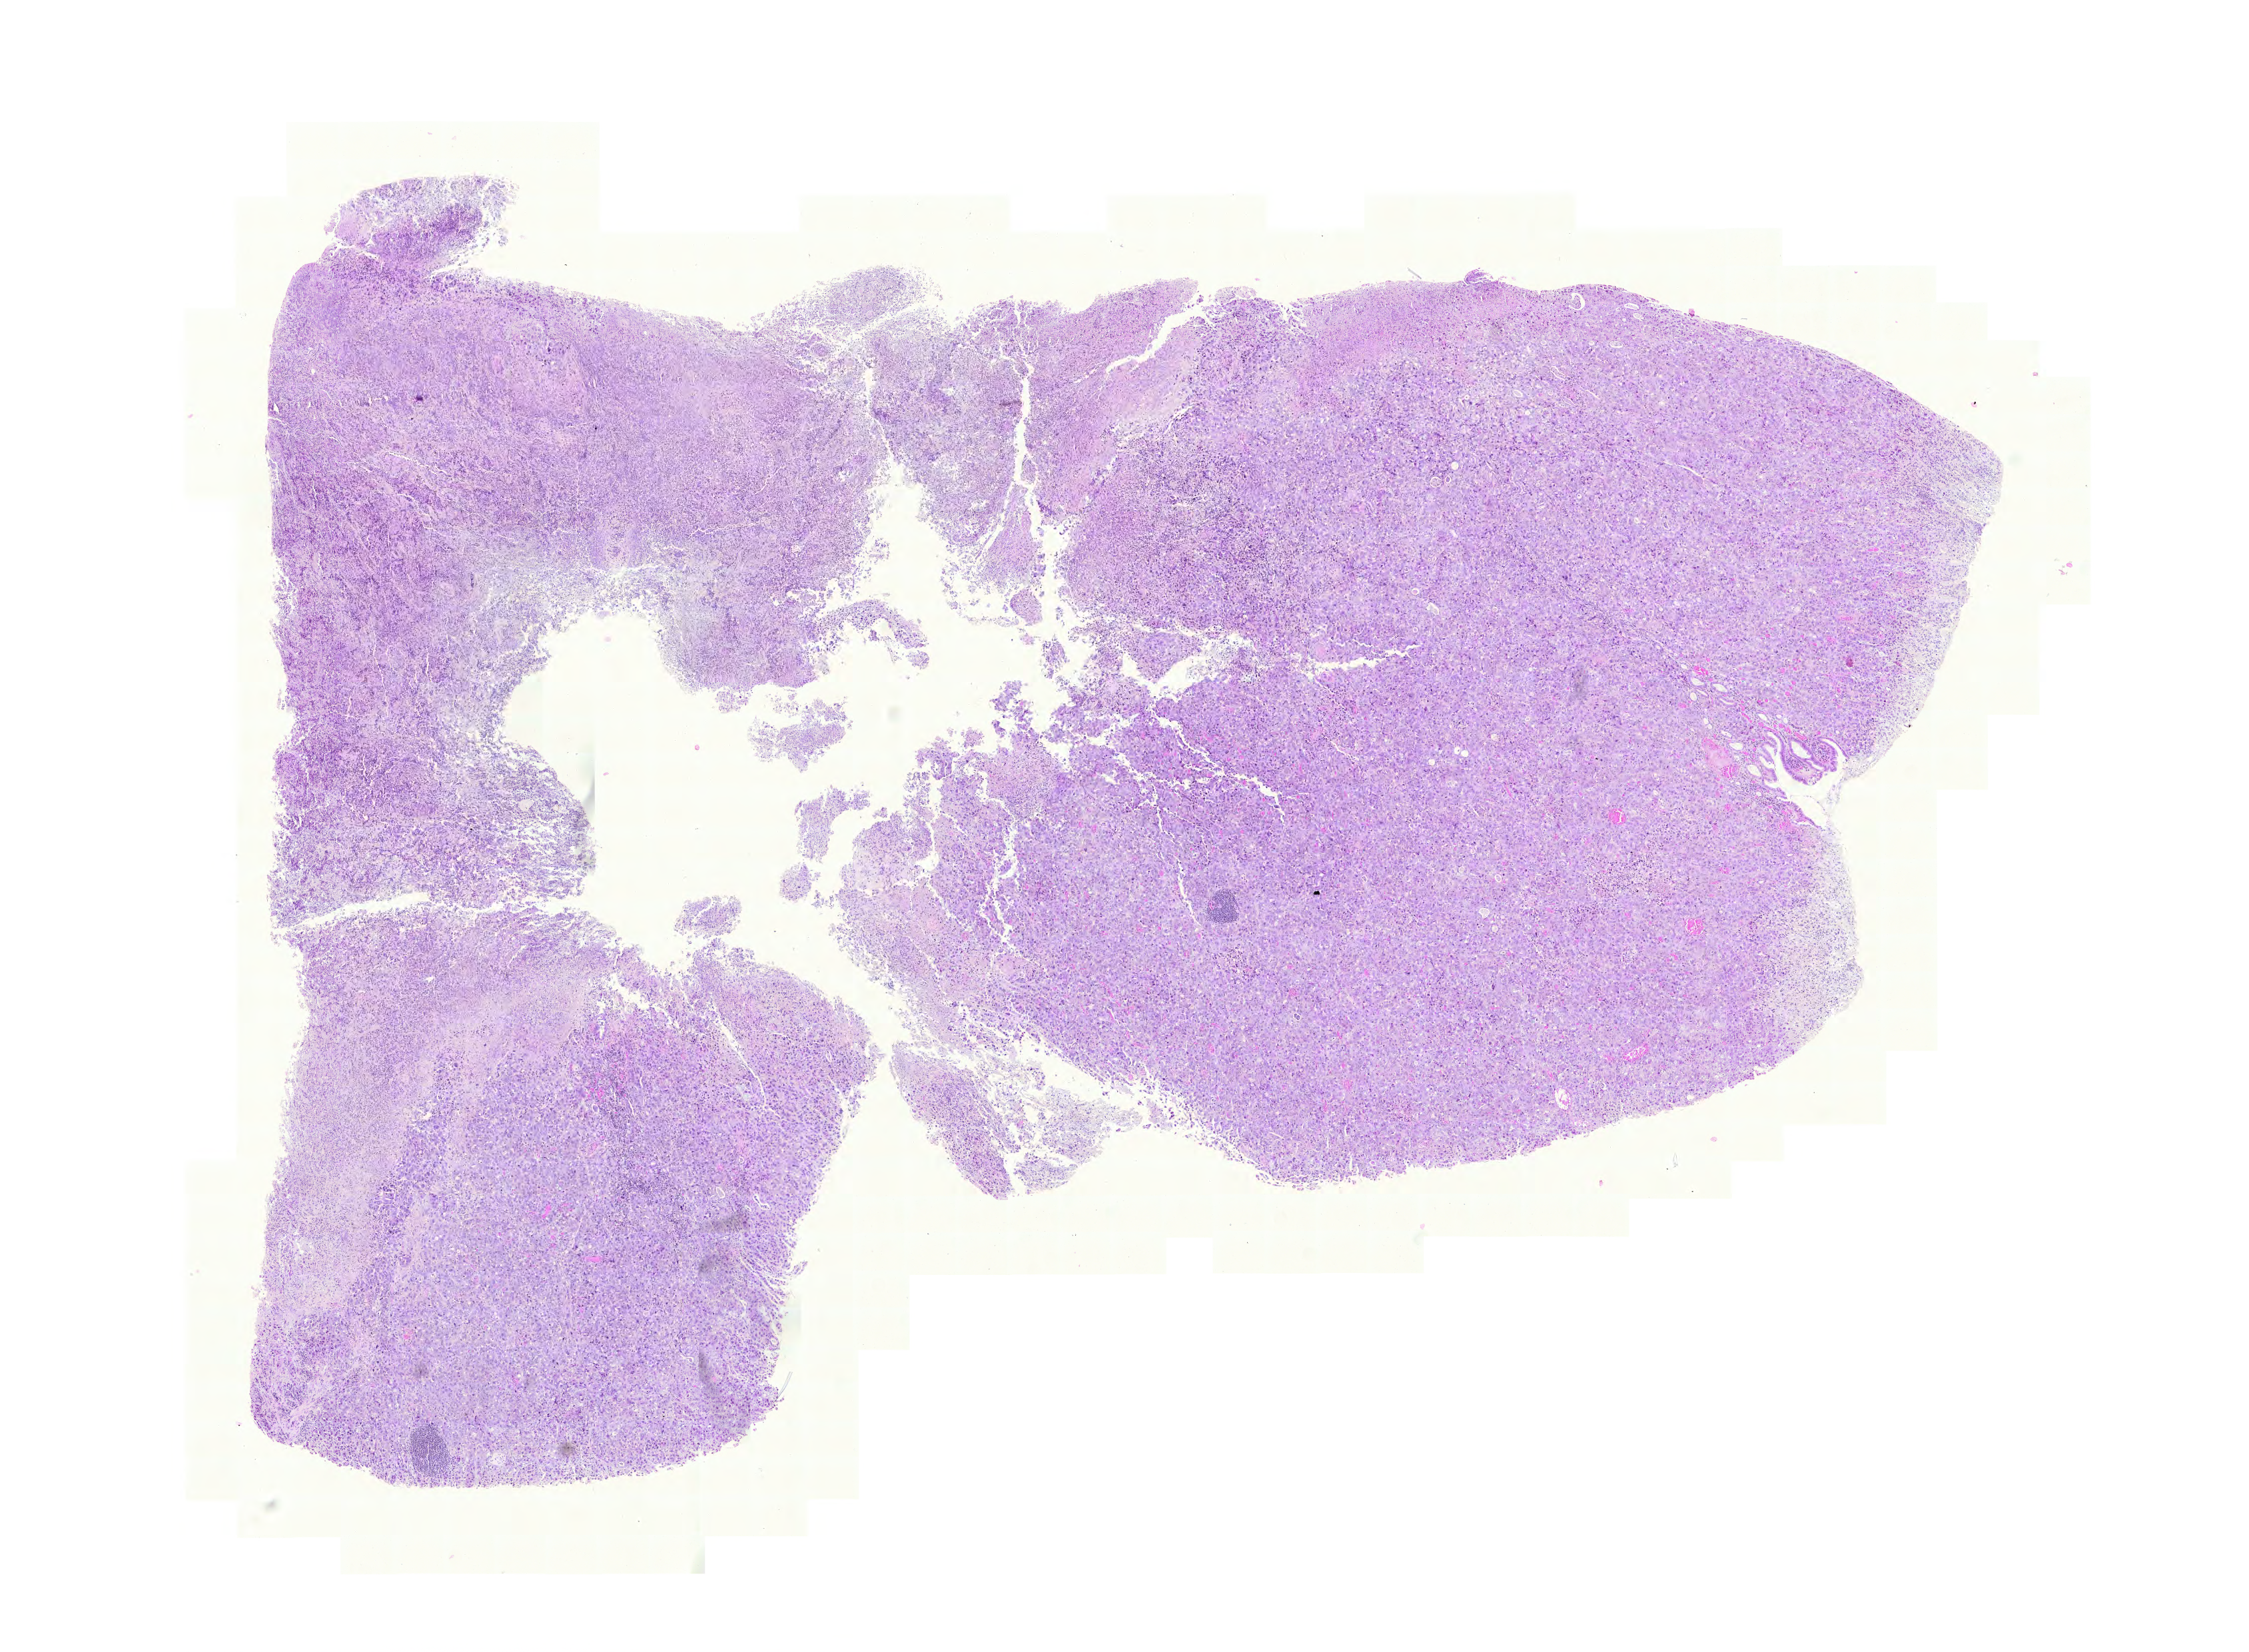
H&E whole-slide image, whole scanned area (about 12.6 x 9.2 mm, from a 20x scan) shown as a low-resolution overview. Formalin-fixed paraffin-embedded (FFPE) diagnostic section. Sample: primary tumour, stomach. Female, age 68 years at initial diagnosis. Histologic grade: G3 (poorly differentiated).
AJCC pathologic stage: IV (5th edition). Diagnosis: Adenocarcinoma, intestinal type (body of stomach).